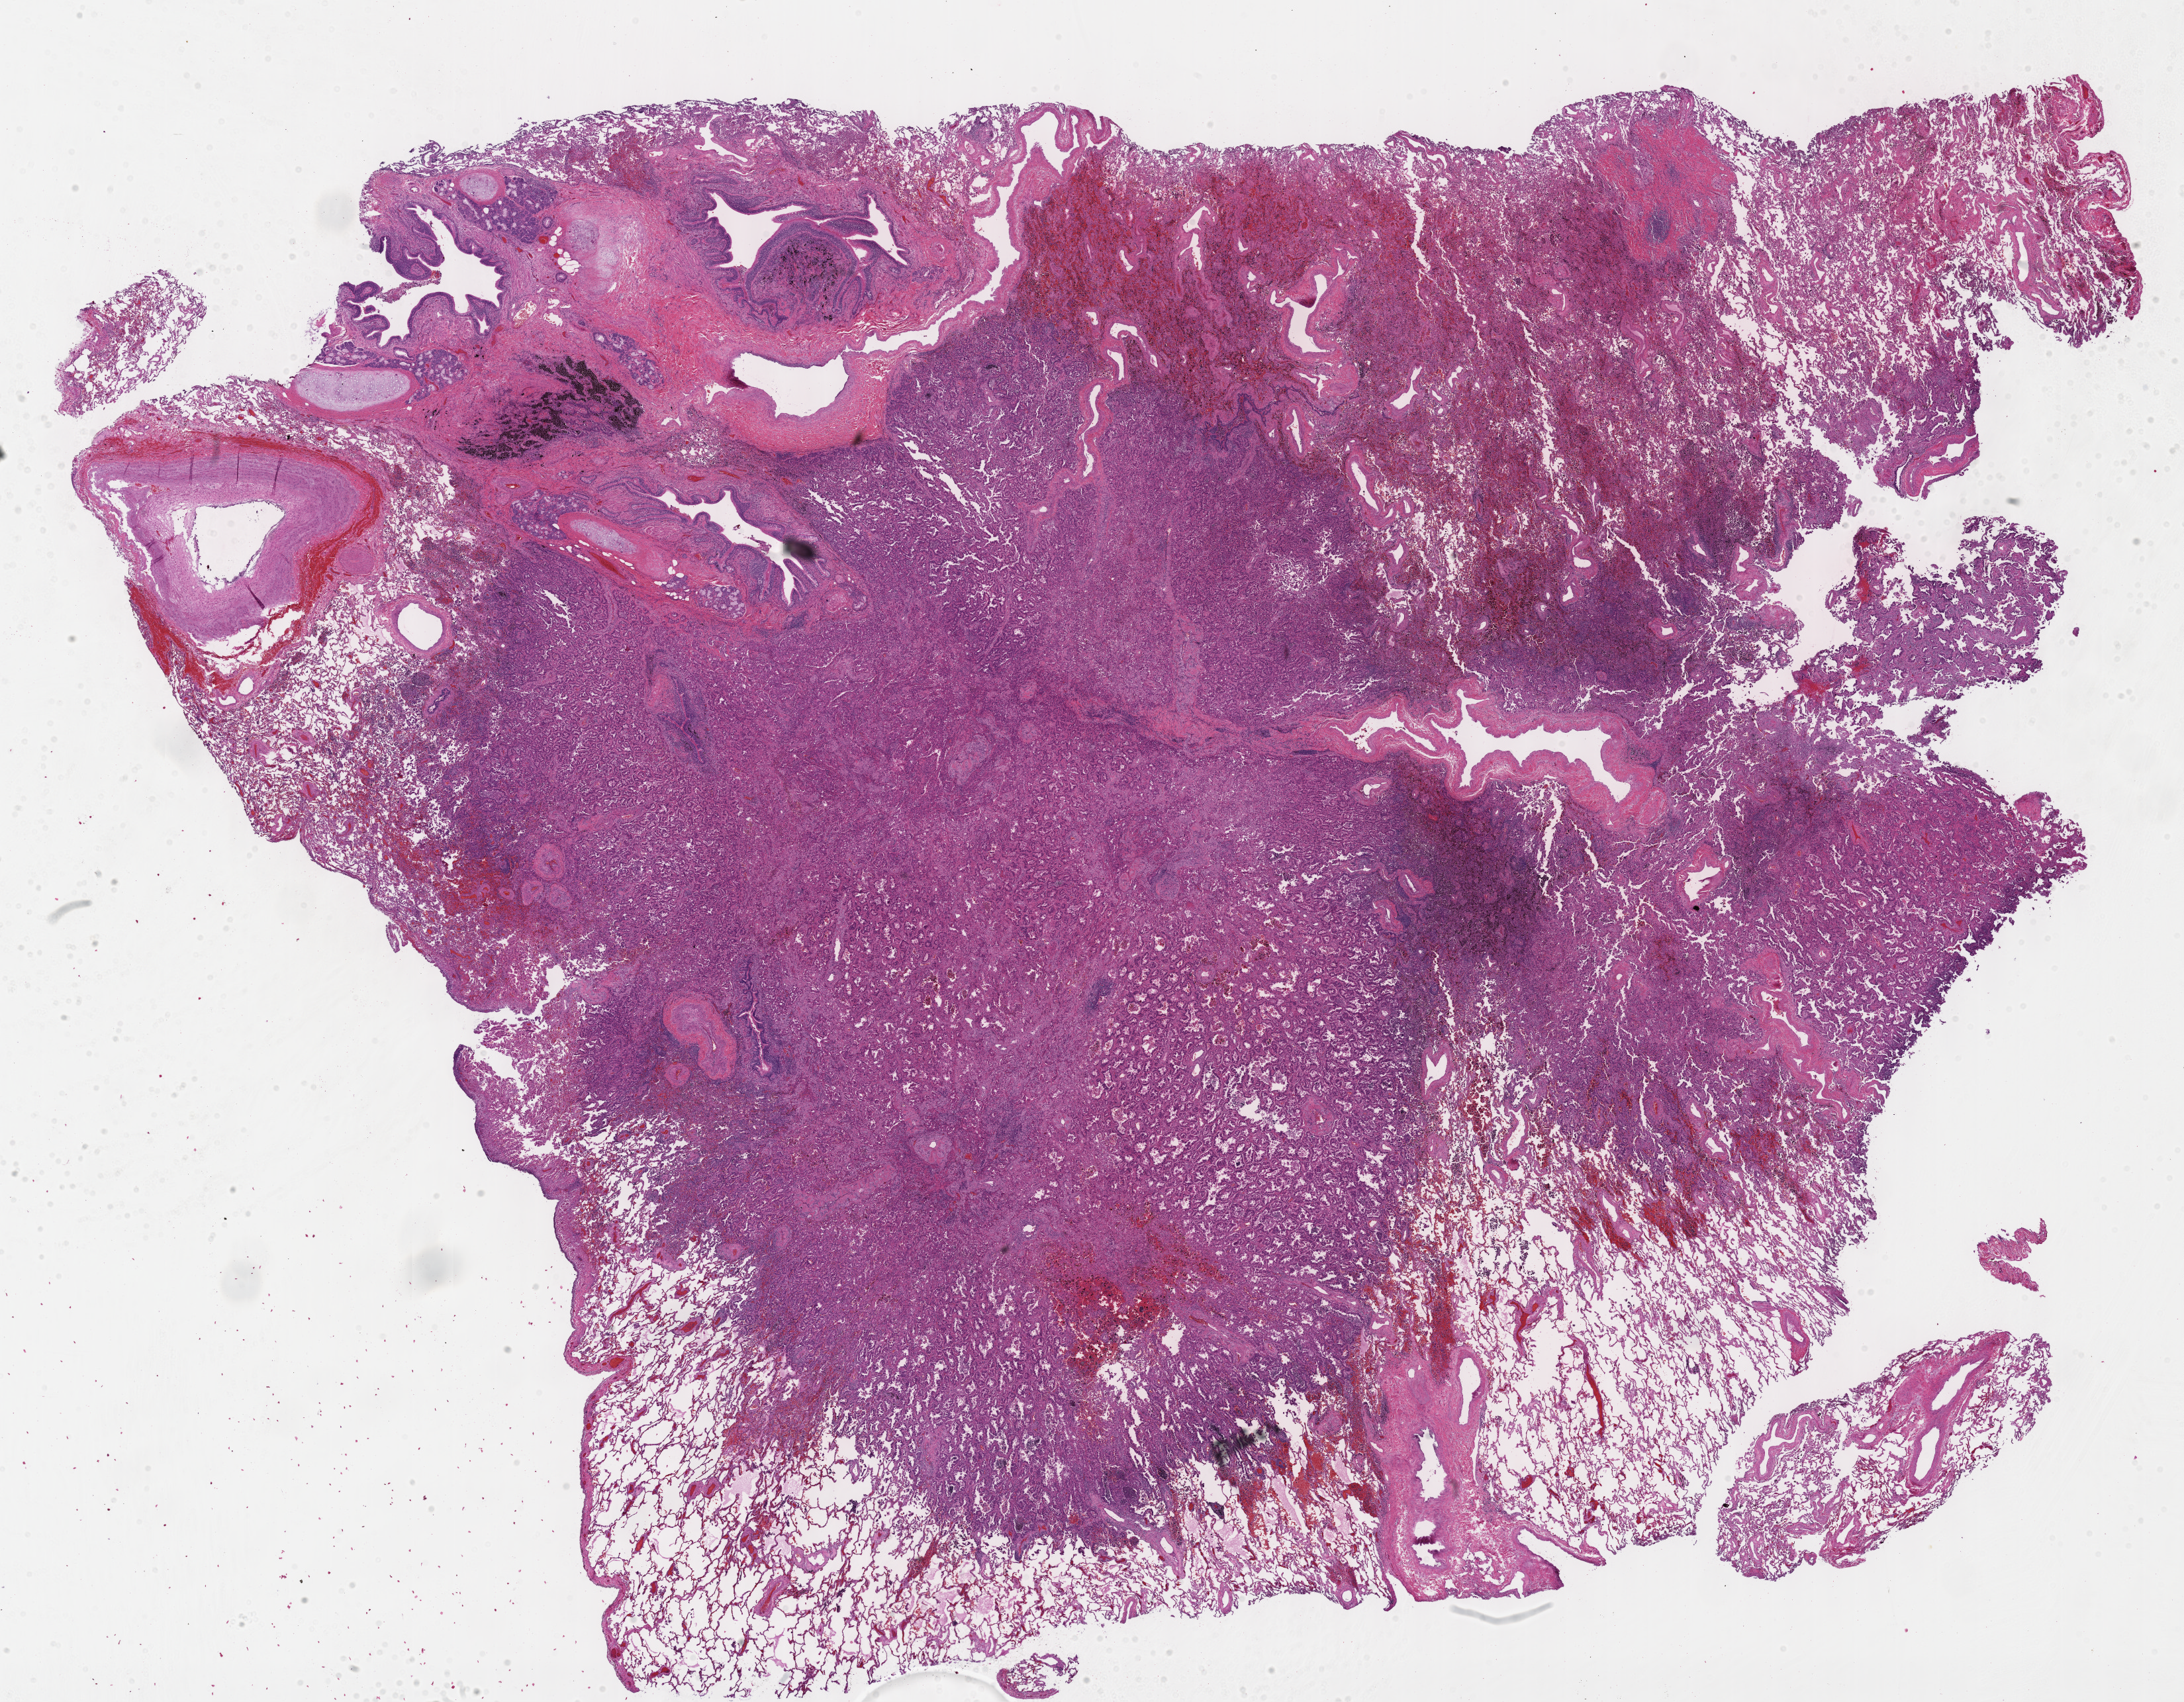
Digitized Hematoxylin and eosin (H&E) stained tissue section (whole slide), whole scanned area (about 26.7 x 20.8 mm, acquisition: 40x scan) shown as a low-resolution overview; formalin-fixed paraffin-embedded (FFPE) diagnostic section; lung, primary tumour sample. Female, age 63 years at initial diagnosis.
* AJCC pathologic stage: II
* laterality: left
* diagnosis: Adenocarcinoma with mixed subtypes (lower lobe, lung)